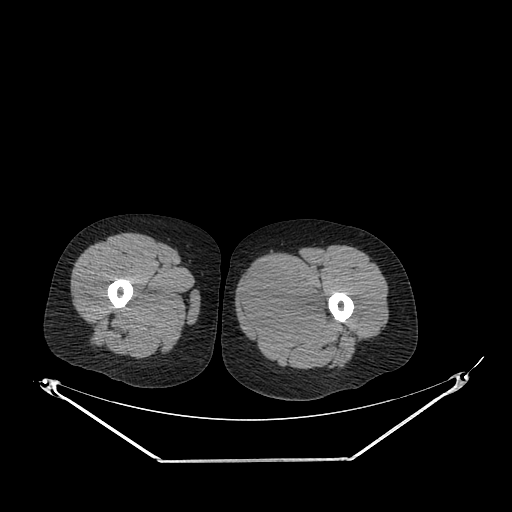
CT of an extremity soft-tissue mass (from a PET/CT study), one axial slice; position 232 of 267 along the scan axis; reconstruction kernel SOFT; 120 kVp; soft-tissue window (W 400 / L 40 HU); 3.75 mm slice thickness; 512 × 512 image matrix, field of view 500 × 500 mm. Female patient. From the clinical record (not read from this slice): histological type: pleiomorphic leiomyosarcoma; grade: intermediate; site of the primary tumour: left thigh.
Outlined on this slice (expert contour drawn on MRI and transferred to this co-registered scan by the dataset authors):
- gross tumour volume including surrounding oedema: bounding box [x1, y1, x2, y2] px = [238, 265, 330, 336]
- gross tumour volume (mass): [240, 267, 325, 334]